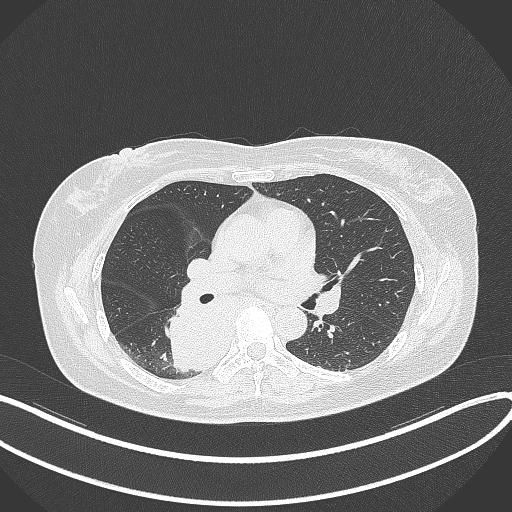
Chest CT, one axial slice; slice 199 of 331 in the series (ordered by position); 120 kVp; lung window (W 1500 / L -600 HU); 1 mm slice thickness; 512 × 512 image matrix, field of view 400 × 400 mm. Female patient, age 54 years. Case-level facts recorded for this patient, not image findings: clinical TNM (as recorded): T4 N0 M0.
Structures marked on this image (bounding box drawn by a radiologist):
- lung tumour (recorded histology: adenocarcinoma): box from (x=160, y=299) to (x=242, y=376) px